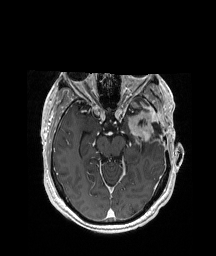
Brain MRI from a brain-tumour surgery series, one axial slice. Position 125 of 208 along the scan axis. T1-weighted post-contrast. 216 × 256 image matrix, field of view 228 × 270 mm. Case-level facts recorded for this patient, not image findings: histopathology: Glioblastoma; WHO grade: 4; IDH mutation: no; tumour location: Left Anterior/Superior Temporal.
Structures marked on this image (expert manual segmentation):
- previous resection cavity: bounding box [x1, y1, x2, y2] px = [139, 119, 161, 134]
- tumour: [123, 100, 158, 144]